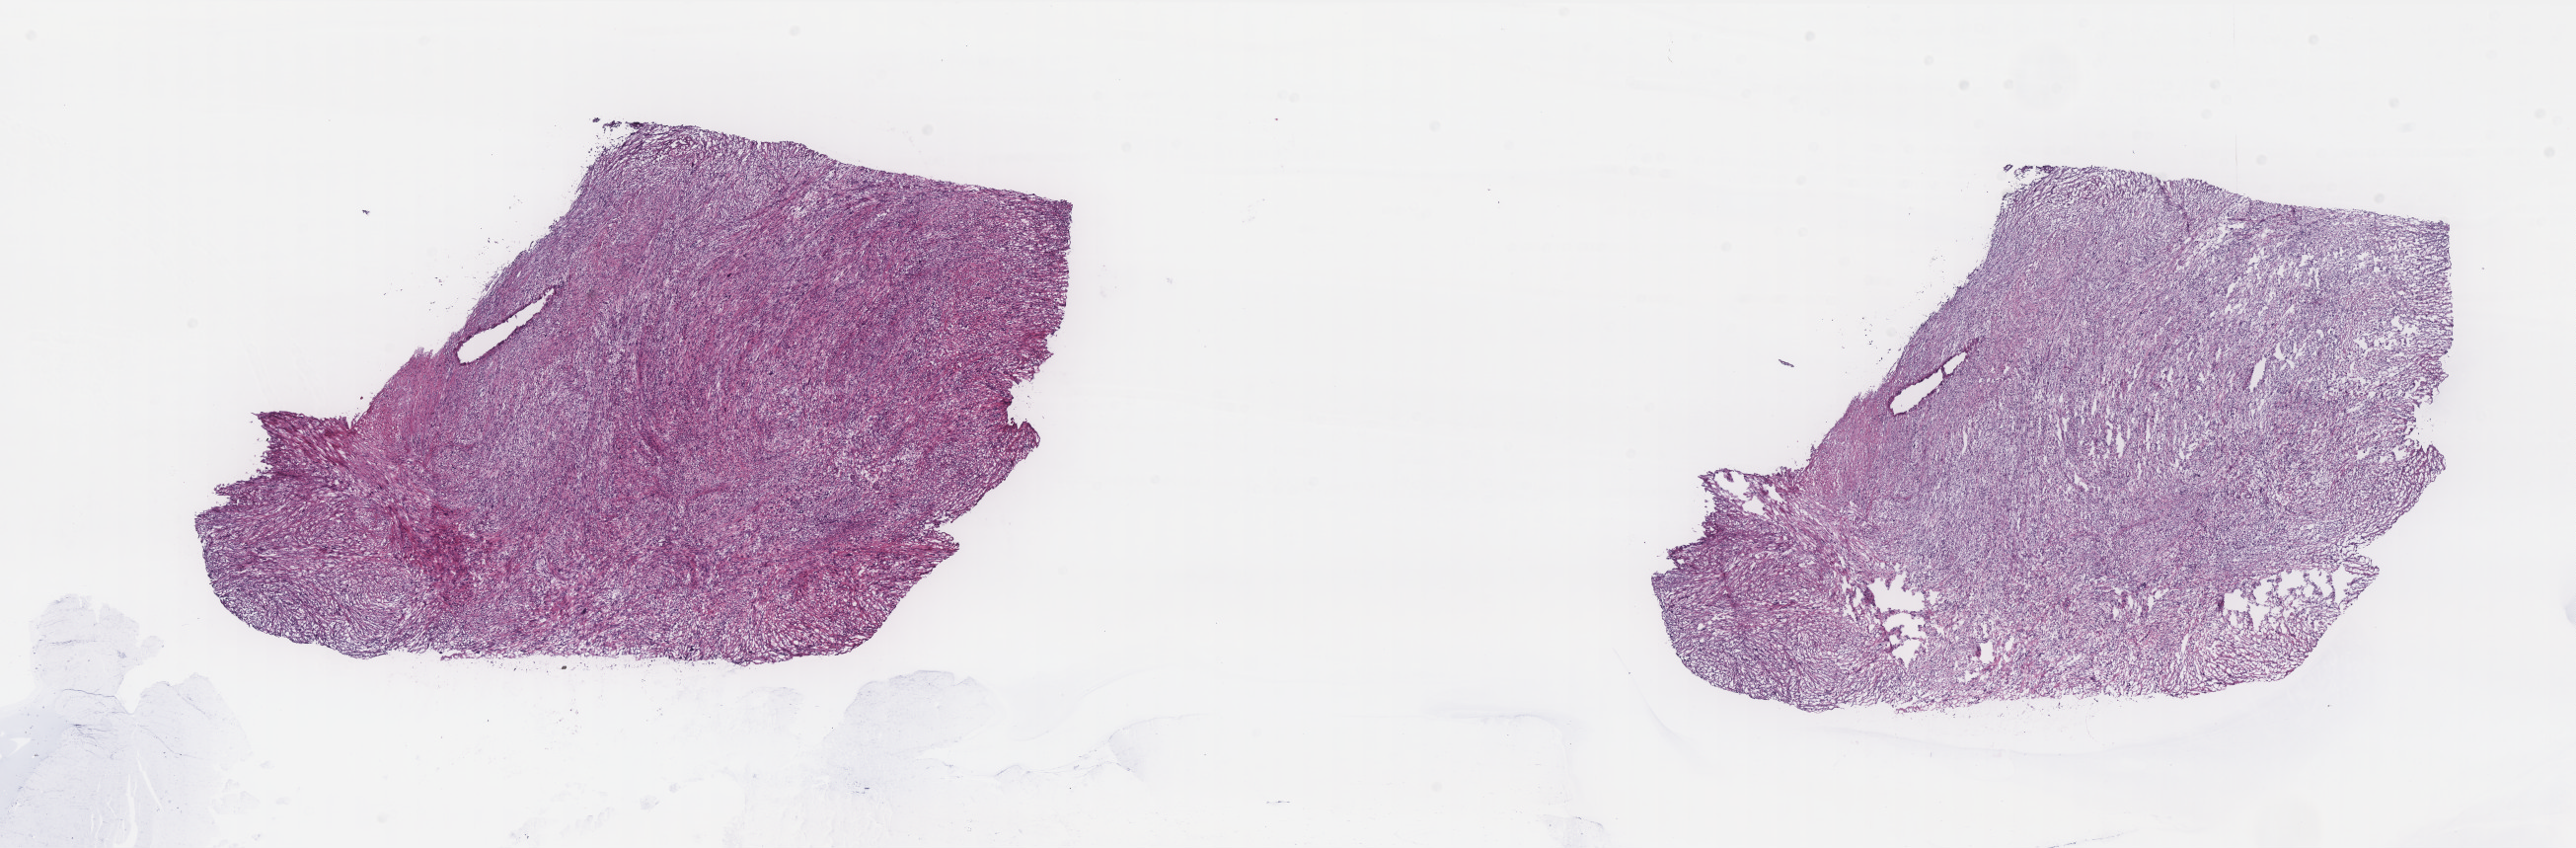
Digitized Hematoxylin and eosin (H&E) stained tissue section (whole slide) — a low-resolution overview of the entire scanned area, about 20.9 x 6.9 mm (acquisition: 40x scan). Frozen section. Primary tumour sample from the retroperitoneum and peritoneum. Male patient; age at initial diagnosis 60 years. Pathologist review of this section (percent, as recorded): tumour cells 80%, tumour nuclei 80%, normal cells 0%, stromal cells 20%, necrosis 0%. Infiltration values recorded for this section: lymphocyte infiltration 3%, monocyte infiltration 1%, neutrophil infiltration 1%.
Diagnosis: Dedifferentiated liposarcoma (retroperitoneum).